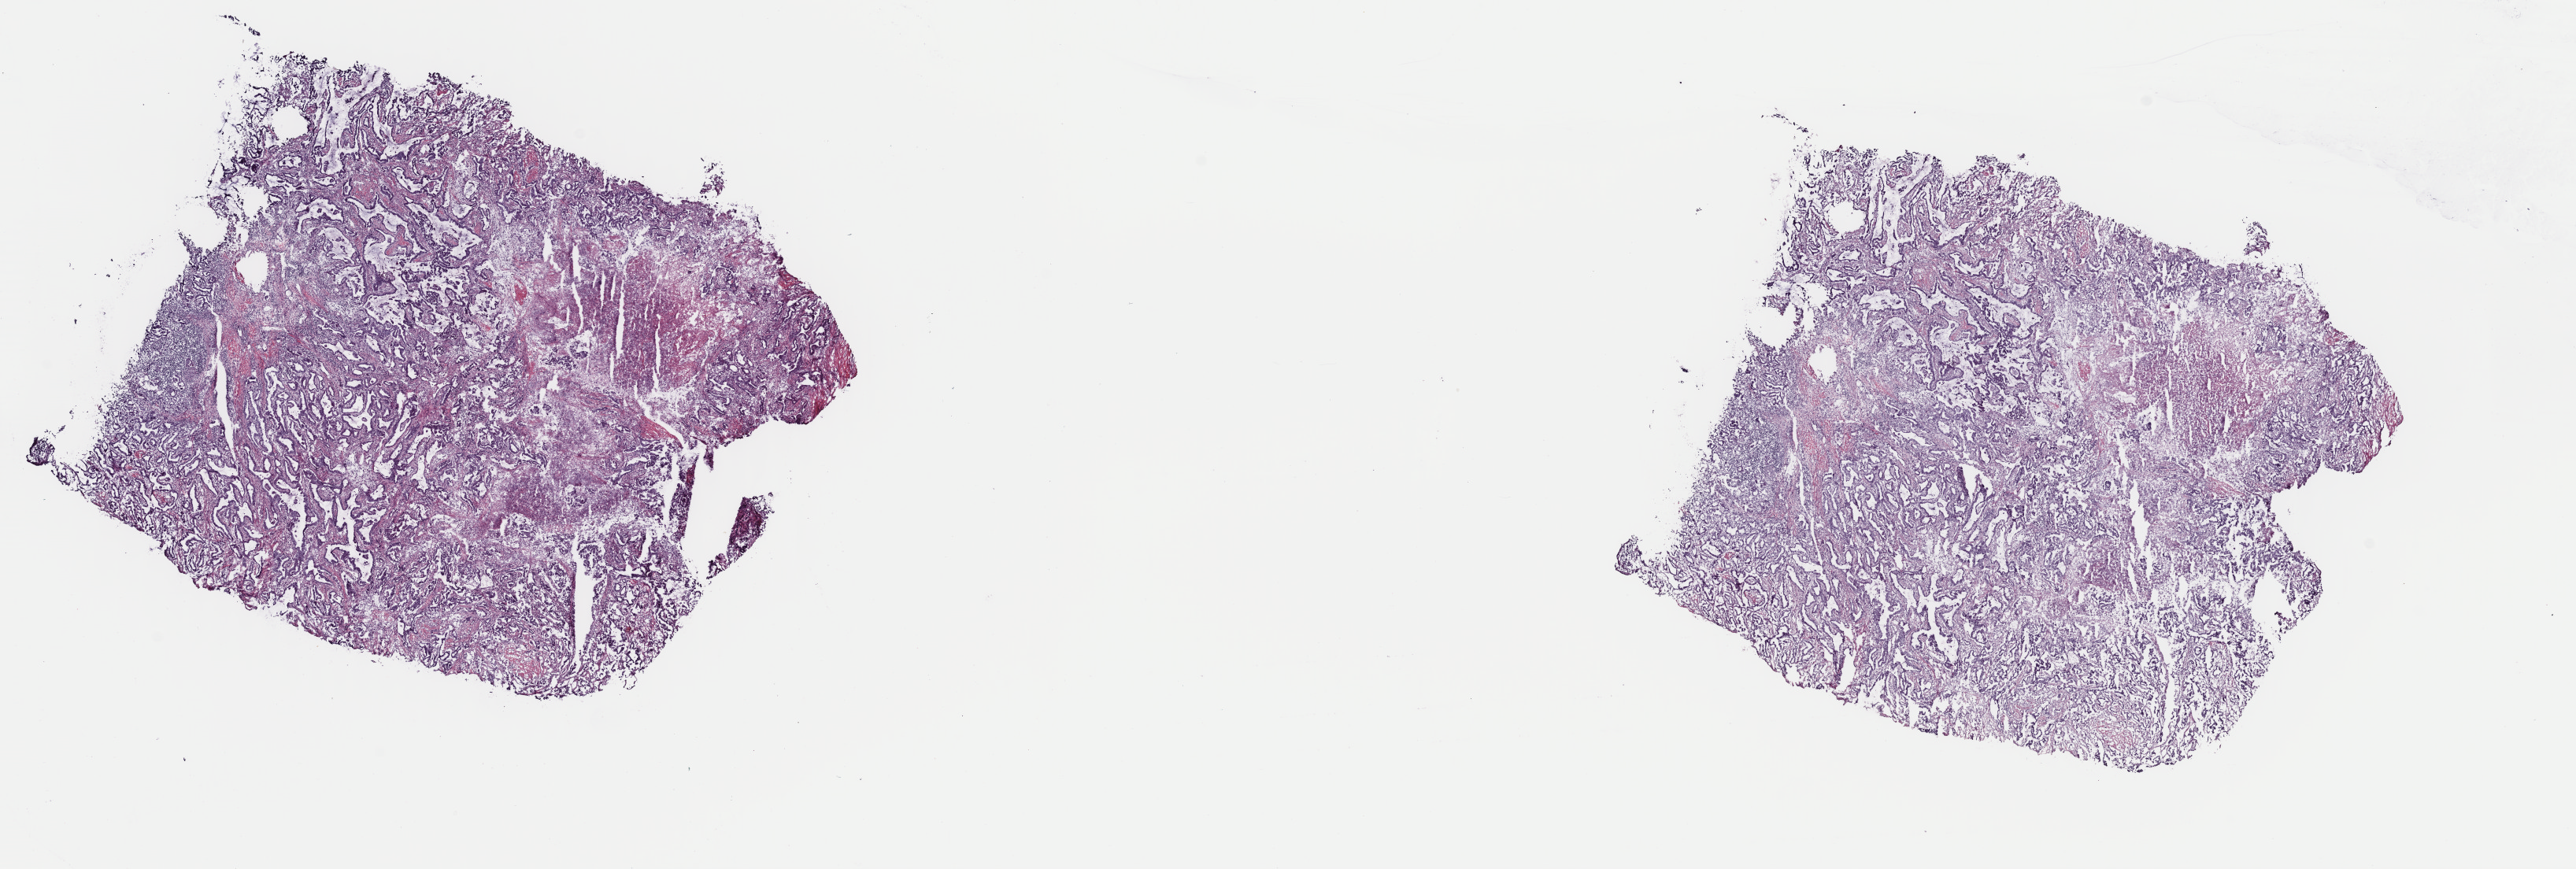
Digitized H&E-stained tissue section (whole slide), low-resolution overview of the scanned area, about 25.8 x 8.7 mm (from a 40x scan), frozen section from the top of the tissue portion, lung, primary tumour sample. Patient: male, age at initial diagnosis 52 years. Composition of this section per pathologist review: tumour cells 82%, tumour nuclei 65%, normal cells 0%, stromal cells 0%, necrosis 18%. Inflammatory infiltration, as recorded: lymphocyte infiltration 5%, monocyte infiltration 3%, neutrophil infiltration 3%.
Diagnosis: Adenocarcinoma with mixed subtypes (lower lobe, lung). AJCC pathologic stage: IB (7th edition). Laterality: right. TNM: T2a N0 M0.